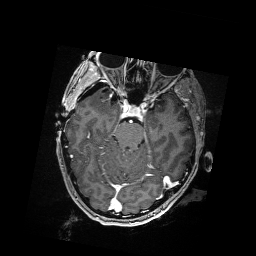
Brain MRI from a brain-tumour surgery series, one axial slice; slice 115 of 176 in the series (ordered by position); T1-weighted post-contrast; 1 mm slice thickness; 256 × 256 image matrix, field of view 256 × 256 mm. Case-level facts recorded for this patient, not image findings: histopathology: Metastatic Carcinoma from Breast primary; tumour location: Right Frontal.
Outlined on this slice (outlined manually by an expert reader):
- residual tumour: bounding box (x1, y1, x2, y2) in pixels: (107, 88, 117, 94)